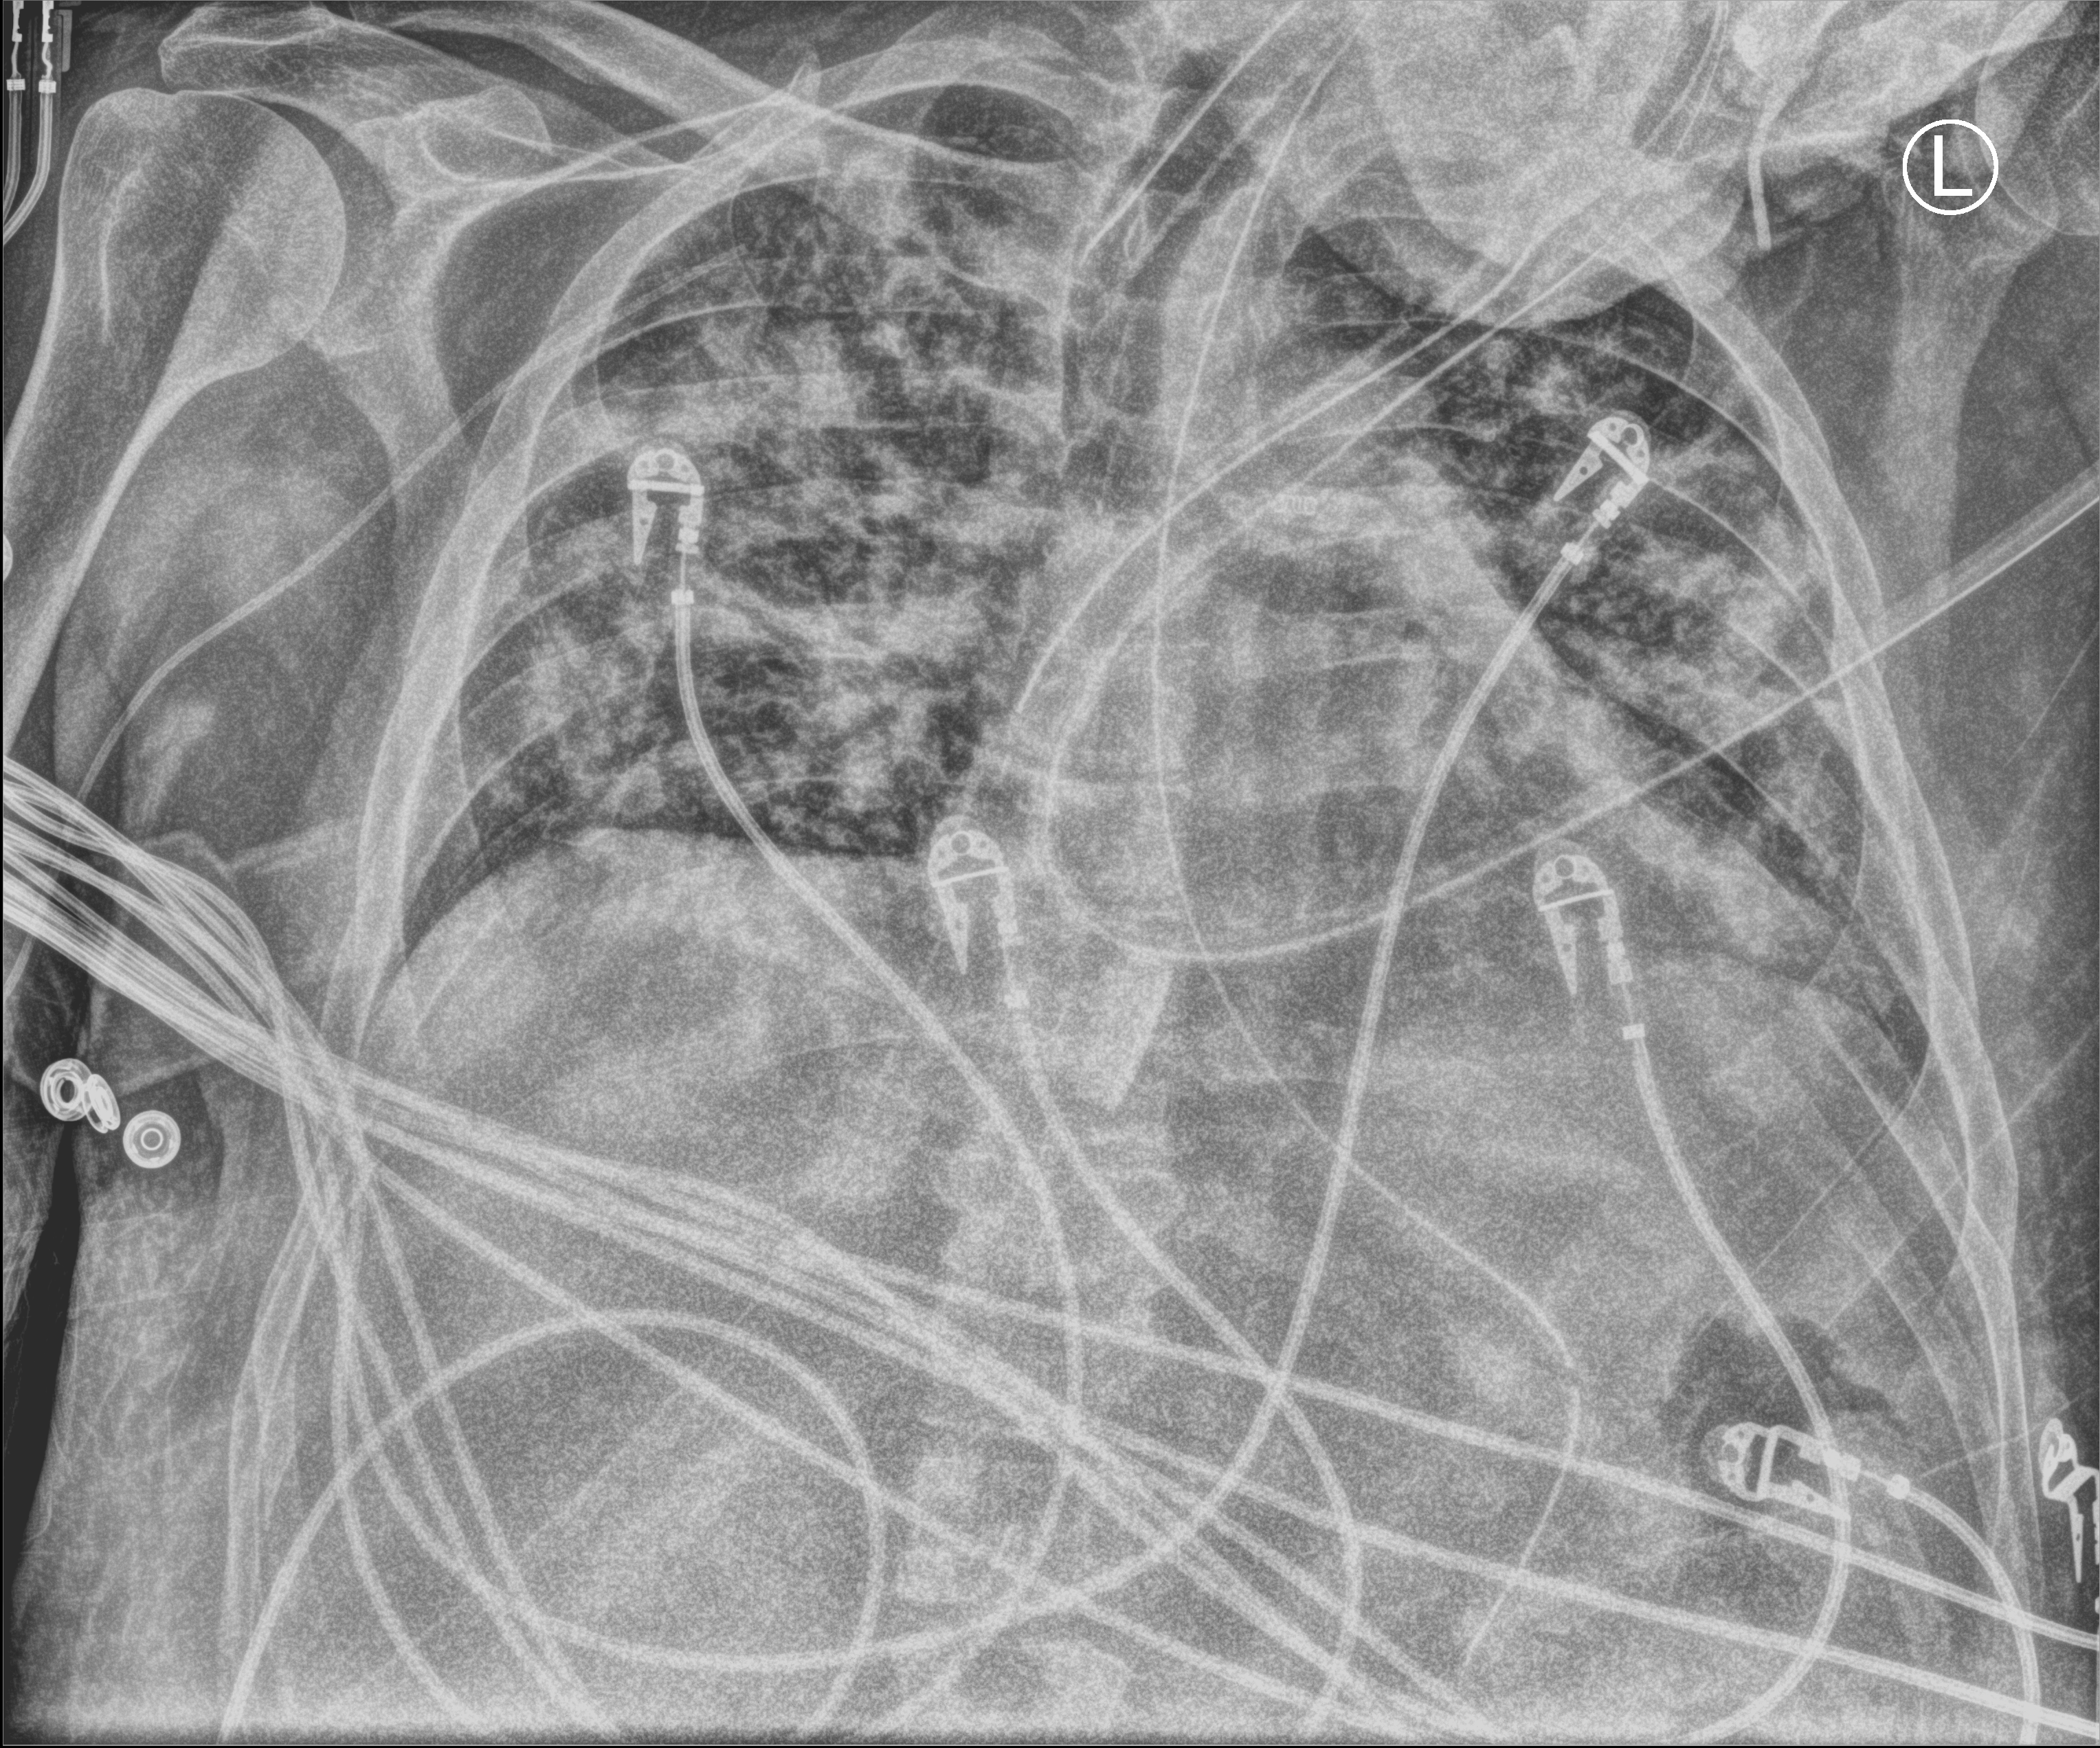
Portable chest radiograph, anteroposterior (AP) projection. Patient hospitalised with COVID-19; male, aged 18–59 years.
From the hospital-stay record, not from the radiograph (when in the stay this image was taken is not recorded): length of hospital stay: 20 days; mechanically ventilated during this hospital stay: yes.